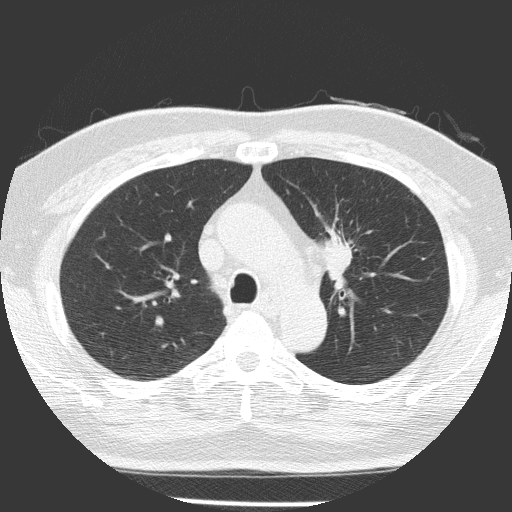
Low-dose screening chest CT, one axial slice. Reconstruction kernel FC51. 120 kVp. Lung window (W 1500 / L -600 HU). 512 × 512 image matrix, field of view 309 × 309 mm.
Annotated regions visible in this slice (manually delineated by an expert):
- lesion 1 (tumor, upper lobe of left lung): bounding box (x1, y1, x2, y2) in pixels: (322, 234, 353, 279)